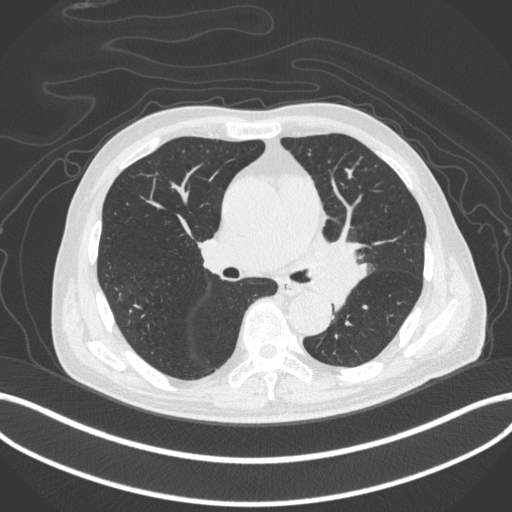
Chest CT, one axial slice; position 249 of 420 along the scan axis; reconstruction kernel B31f; 120 kVp; lung window (W 1500 / L -600 HU); 512 × 512 image matrix. Male patient, age 77 years. From the clinical record (not read from this slice): clinical TNM (as recorded): T3 N1 M0.
Annotated regions visible in this slice (rectangle marked by the reading radiologist):
- lung tumour (recorded histology: adenocarcinoma): bounding box (x1, y1, x2, y2) in pixels: (305, 237, 365, 309)